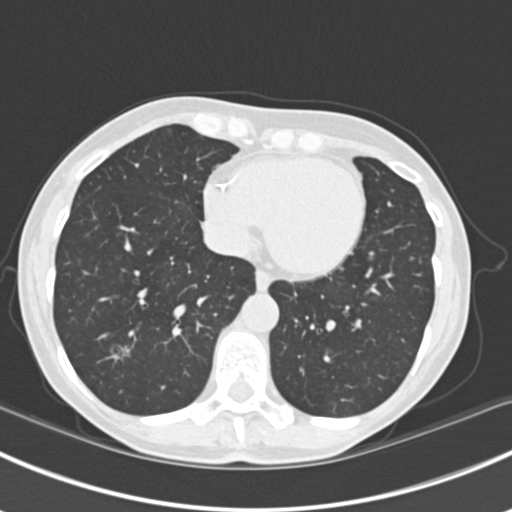
Chest CT (low-dose screening protocol), one axial image, first (baseline) screen, lung window (W 1500 / L -600 HU), slice 133 of 224 in the series, 512 × 512 image matrix. Female, age 63 years at enrolment.
Expert reader's lesion annotation, bounding box [x1, y1, x2, y2] px = [96, 322, 146, 369]. The screening reader recorded 10 non-calcified nodules or masses ≥4 mm on this exam (right lower lobe, right lower lobe, left lower lobe, left lower lobe, right middle lobe, right lower lobe, left lower lobe, left upper lobe, right upper lobe, left upper lobe); which of them this box marks is not recorded. Official screen result: positive, change unspecified: nodule(s) >= 4 mm or enlarging nodule(s), mass(es), or other non-specific abnormalities suspicious for lung cancer. Lung cancer was diagnosed 751 days after this screen (after the third annual screen): bronchiolo-alveolar adenocarcinoma, NOS, right upper lobe, right middle lobe, right lower lobe, left upper lobe, left lower lobe, moderately differentiated (G2), stage IV (AJCC 6th edition).